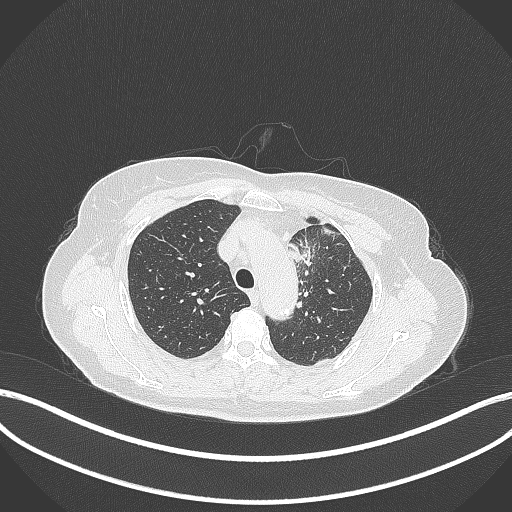
Chest CT, one axial slice. Position 257 of 369 along the scan axis. Reconstruction kernel B70f. 120 kVp. Lung window (W 1500 / L -600 HU). 1 mm slice thickness. 512 × 512 image matrix. Female patient, age 65 years. From the clinical record (not read from this slice): clinical TNM (as recorded): T2a N0 M0.
Annotated regions visible in this slice (rectangle marked by the reading radiologist):
- lung tumour (recorded histology: adenocarcinoma): box from (x=281, y=235) to (x=314, y=269) px